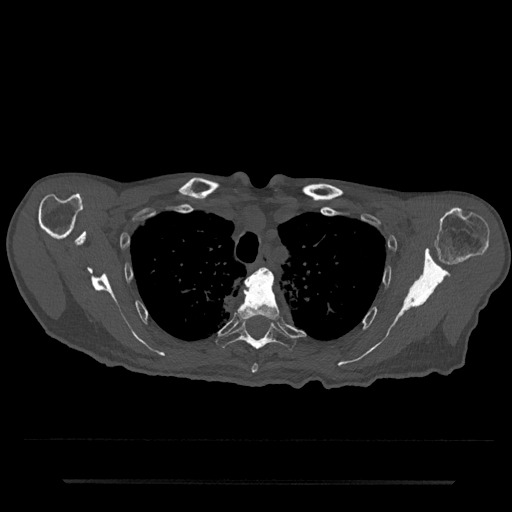
CT including the spine, one axial slice; slice 601 of 797 in the series (ordered by position); bone window (W 1800 / L 400 HU); 0.5 mm slice thickness; 512 × 512 image matrix. Patient: male, 74 years. From the clinical record (not read from this slice): primary cancer: prostate.
Annotated regions visible in this slice (semi-automatic segmentation, software-assisted and operator-edited):
- T3 vertebra: bounding box (x1, y1, x2, y2) in pixels: (264, 268, 273, 277)
- T4 vertebra: (237, 269, 280, 373)
- T5 vertebra: (216, 318, 297, 351)